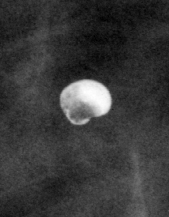
Cropped region of a digitized screen-film mammogram centred on a radiologist-marked abnormality, left breast, CC view.
Finding: calcifications, morphology vascular / coarse / lucent centered; BI-RADS assessment category 2; benign; no additional work-up was recommended (benign without callback).